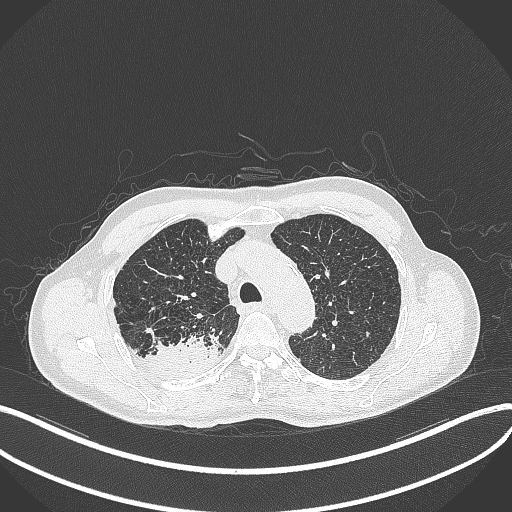
Chest CT, one axial slice; slice 335 of 428 in the series (ordered by position); reconstruction kernel B70f; lung window (W 1500 / L -600 HU); 1 mm slice thickness; 512 × 512 image matrix, field of view 400 × 400 mm. Male patient, age 79 years. Case-level facts recorded for this patient, not image findings: clinical TNM (as recorded): T3 N0 M0.
Outlined on this slice (bounding box drawn by a radiologist):
- lung tumour (recorded histology: adenocarcinoma): bounding box <141,332,223,374> (left, top, right, bottom; pixels)